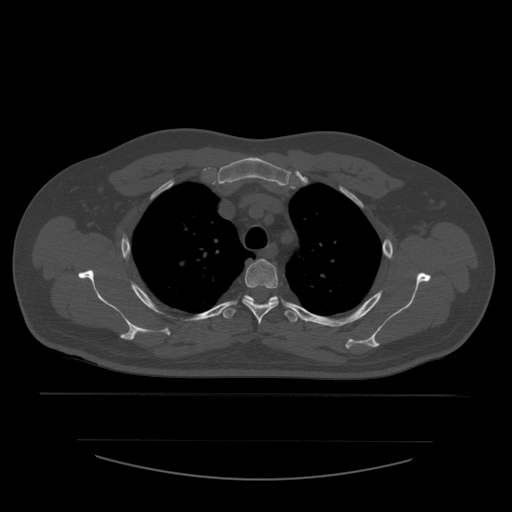
CT including the spine, one axial slice; position 430 of 532 along the scan axis; reconstruction kernel STANDARD; bone window (W 1800 / L 400 HU); 1.25 mm slice thickness; 512 × 512 image matrix, field of view 441 × 441 mm. Patient age 44 years. From the clinical record (not read from this slice): primary cancer: soft tissue sarcoma.
Outlined on this slice (semi-automatically segmented with operator editing):
- T3 vertebra: bounding box (x1, y1, x2, y2) in pixels: (242, 259, 279, 325)
- T4 vertebra: (223, 295, 298, 323)